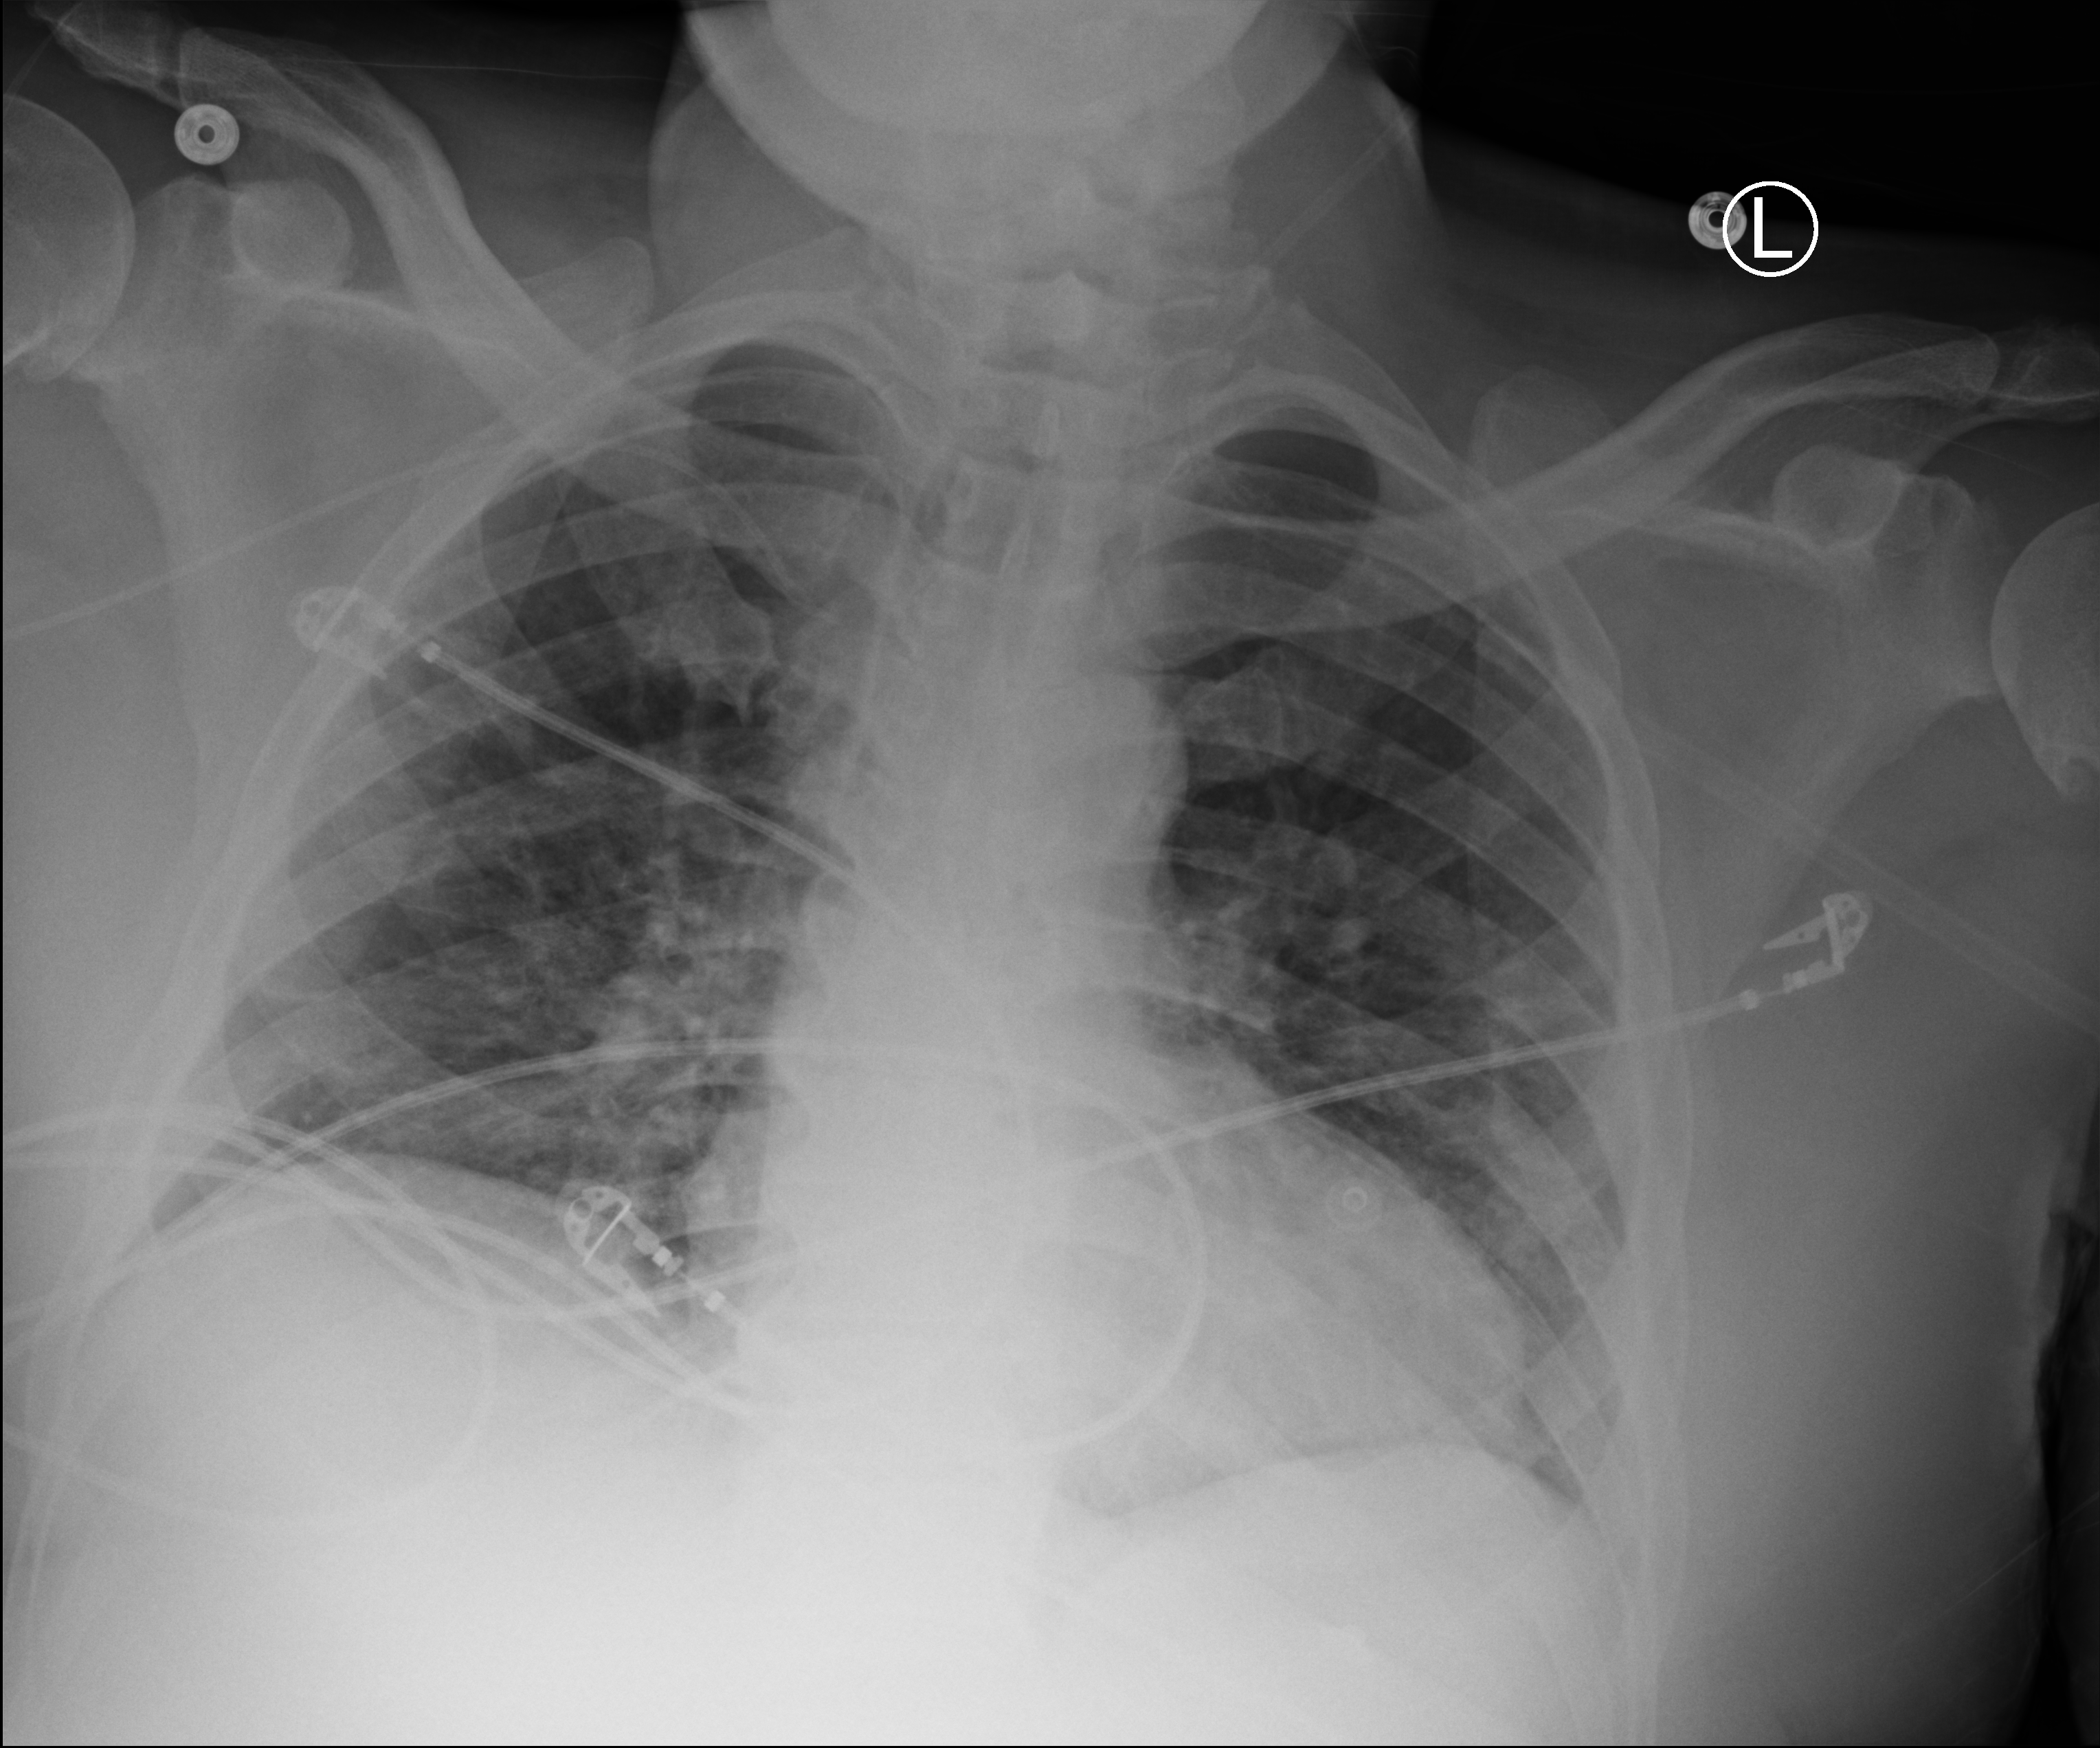
Chest X-ray (portable). Male patient hospitalised with COVID-19, age 18–59 years.
Hospital-stay facts (about this admission, not read from this image; timing relative to this image not recorded): length of hospital stay: 41 days; admitted to intensive care during this hospital stay: yes.